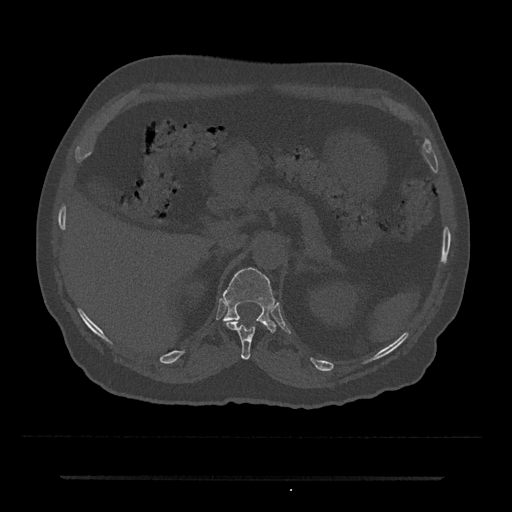
CT including the spine, one axial slice. Position 148 of 797 along the scan axis. Reconstruction kernel Br40s/3. 120 kVp. Bone window (W 1800 / L 400 HU). 512 × 512 image matrix, field of view 437 × 437 mm. Male patient, age 69 years. Case-level facts recorded for this patient, not image findings: primary cancer: prostate.
Outlined on this slice (semi-automatically segmented with operator editing):
- T11 vertebra: bounding box [x1, y1, x2, y2] px = [226, 321, 256, 360]
- T12 vertebra: [222, 267, 276, 332]